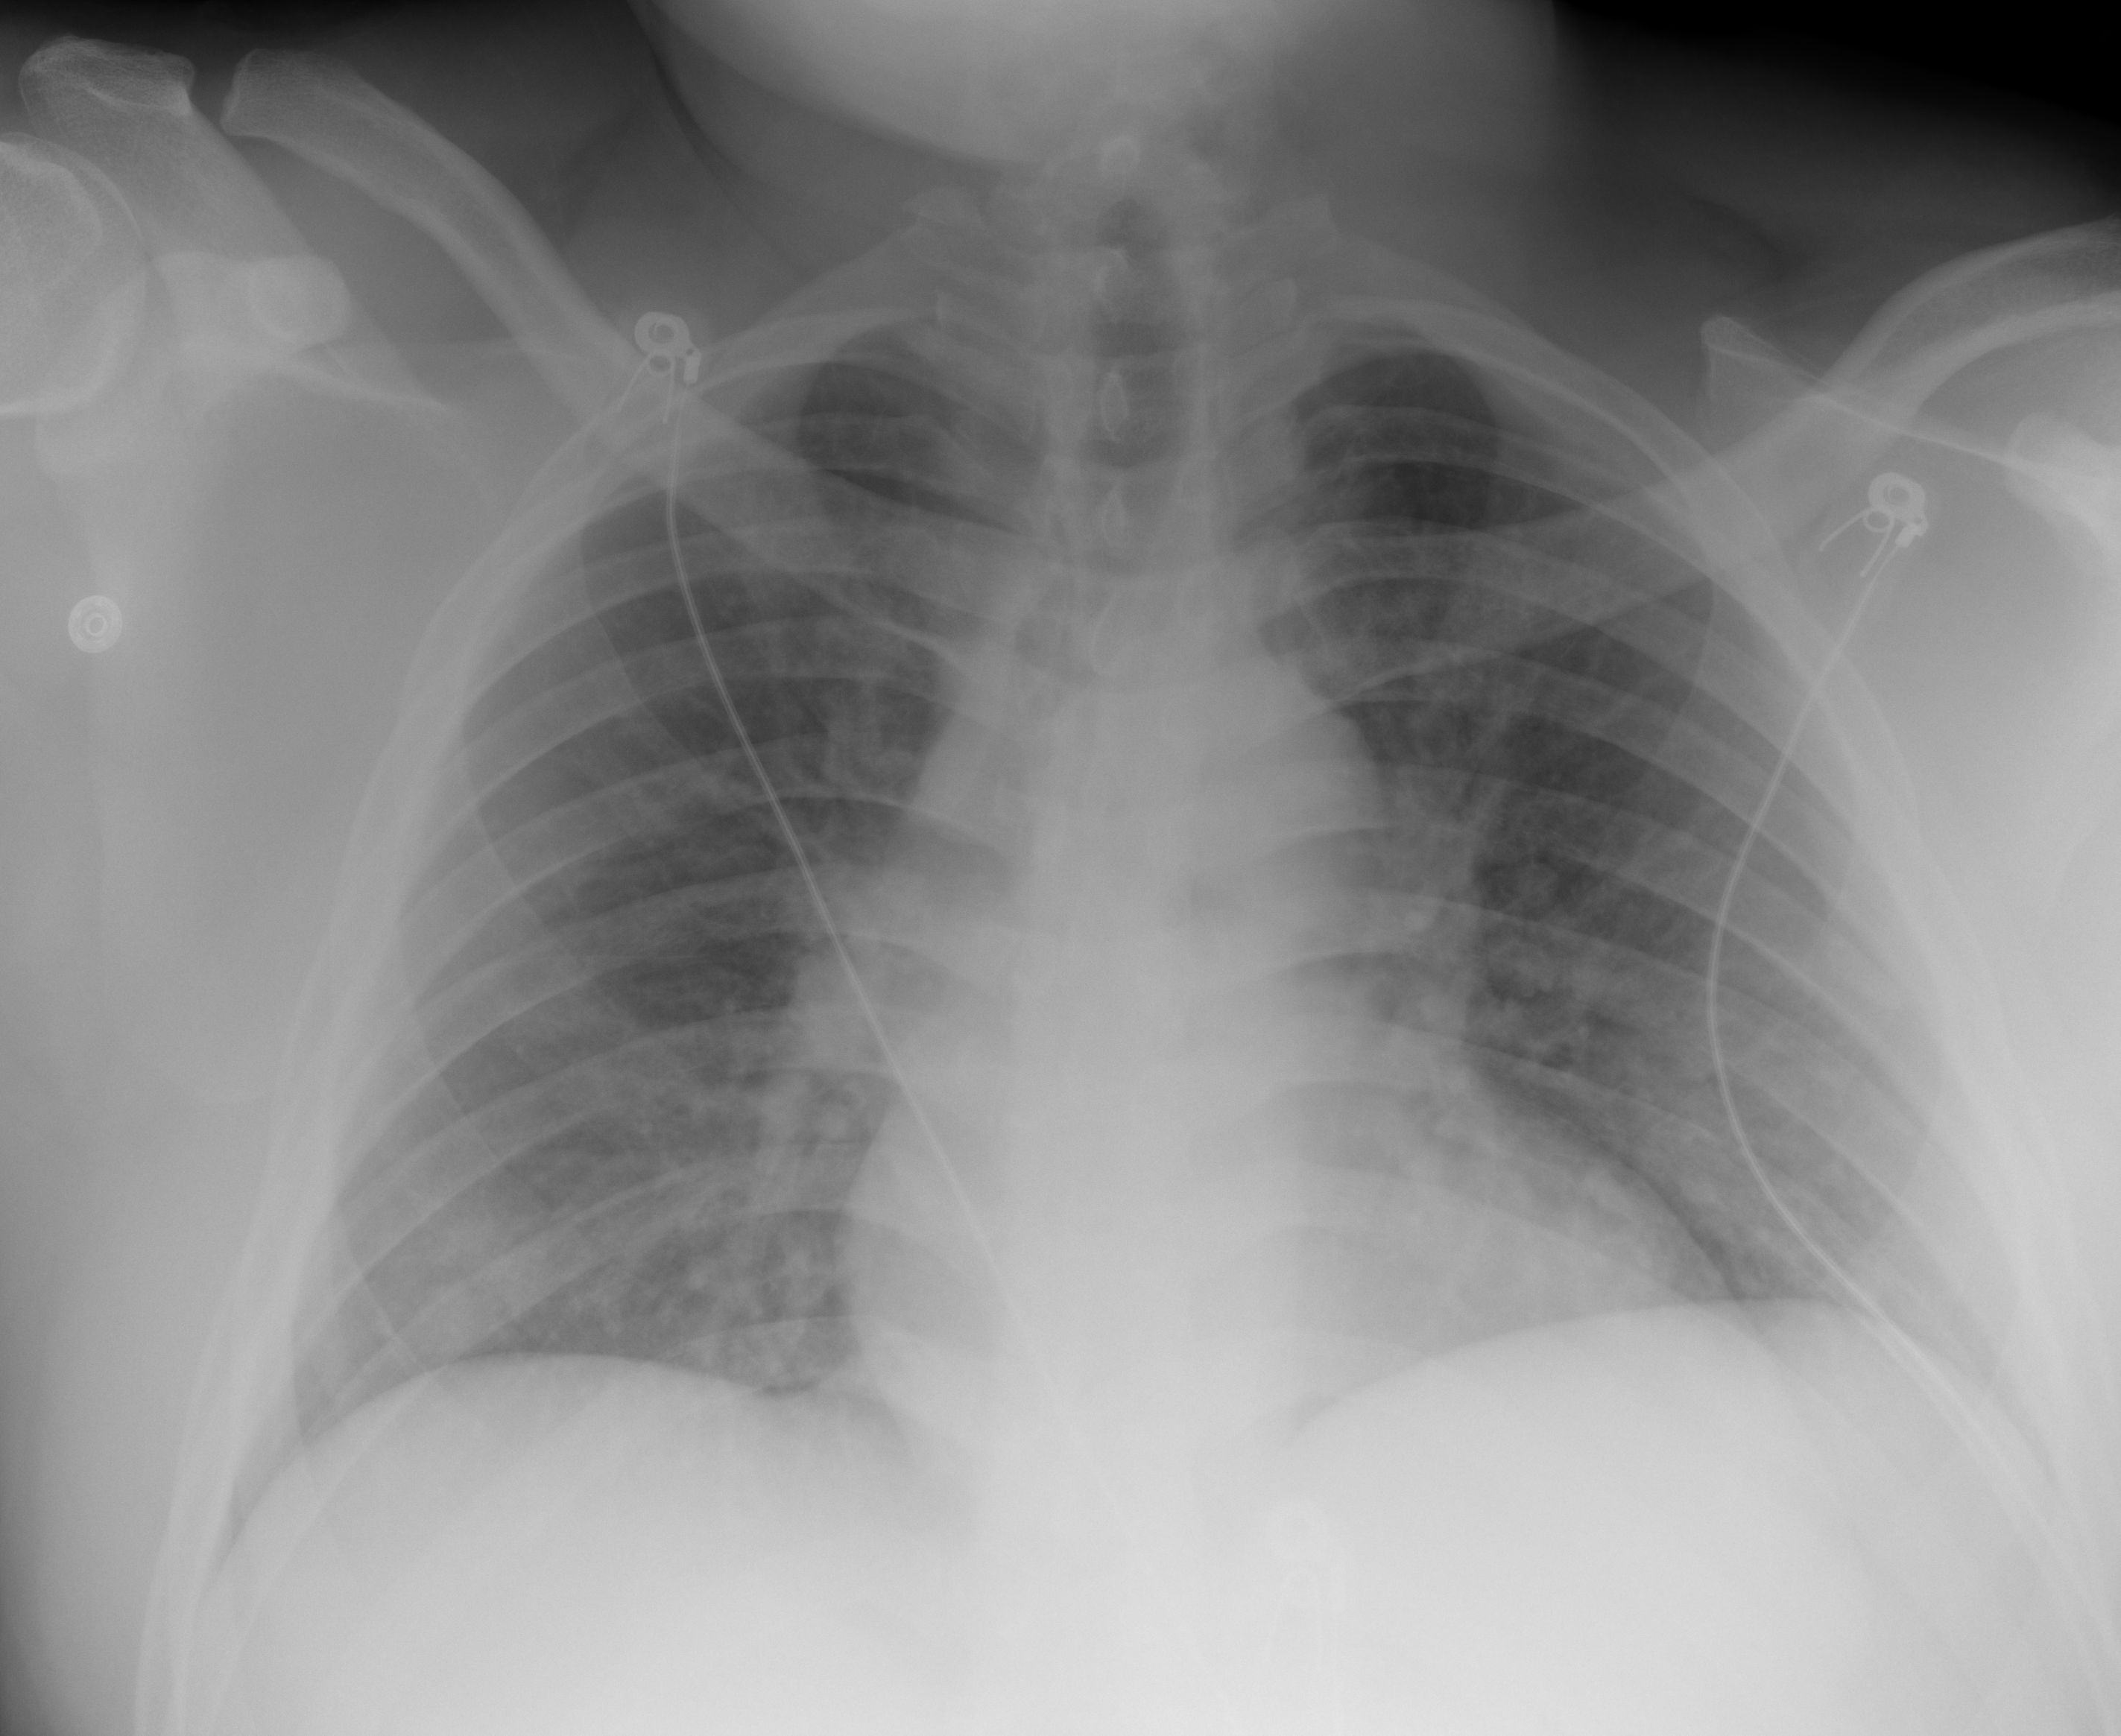
Chest X-ray (portable), AP projection. Male patient, age 36 years; imaged 0 days after the COVID-19 diagnosis.
Key findings recorded by the radiologist: No focal consolidation or pleural effusion.